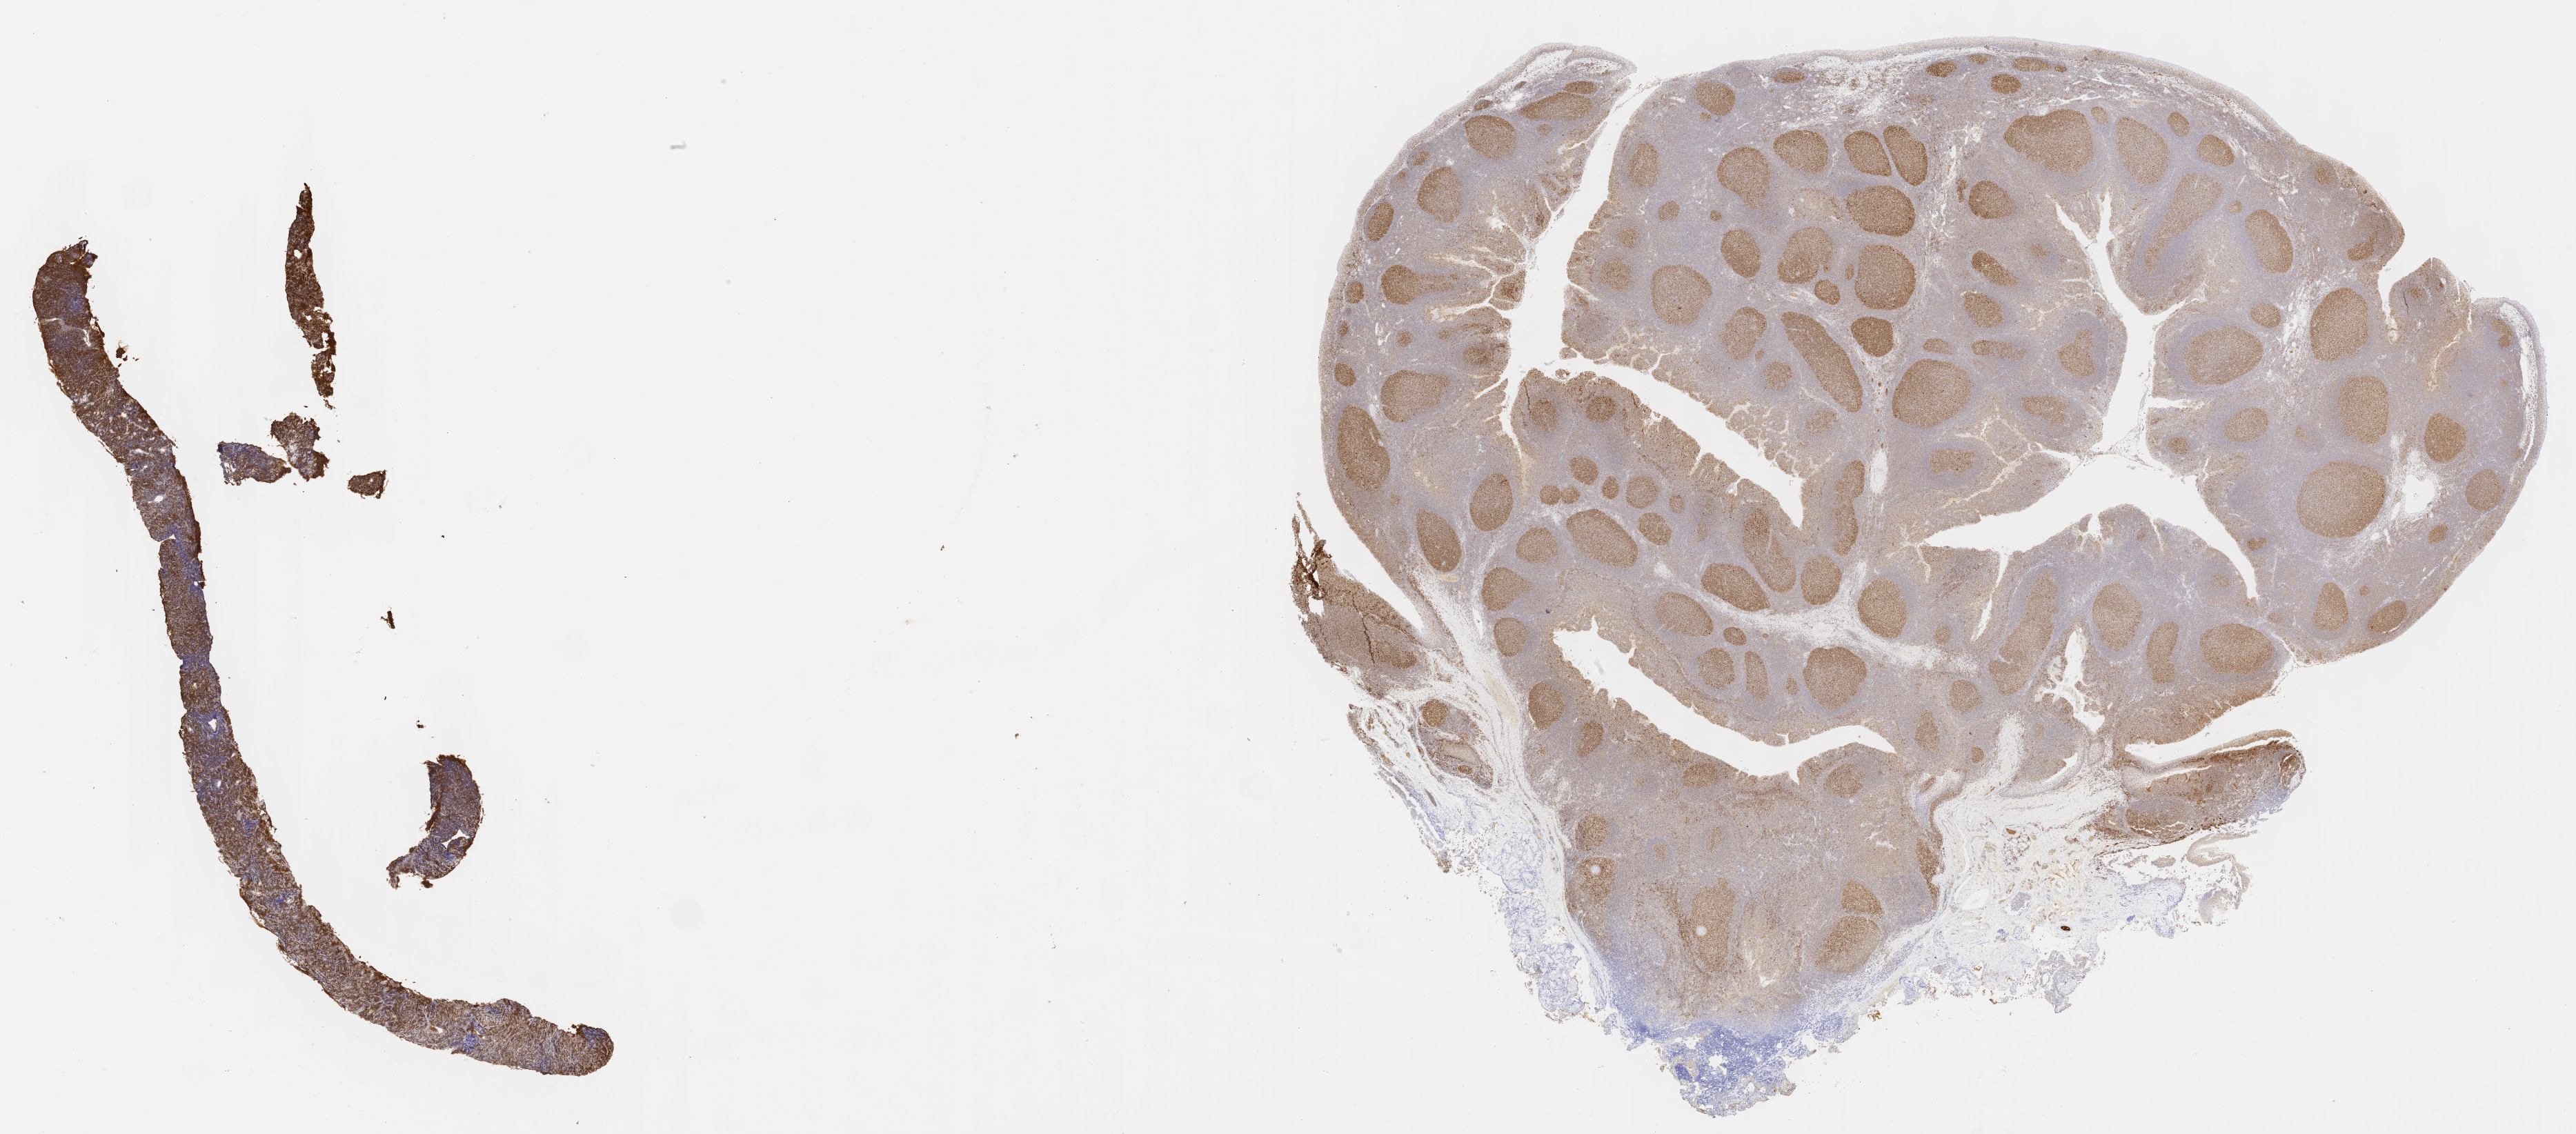
Immunohistochemistry (IHC) whole-slide image stained for BCL6 — a low-resolution overview of the entire scanned area, about 30.2 x 13.3 mm, specimen: tumor tissue, anatomic site: ovary. Female patient; age at initial diagnosis 9 years.
Histologic diagnosis: Burkitt lymphoma, NOS.